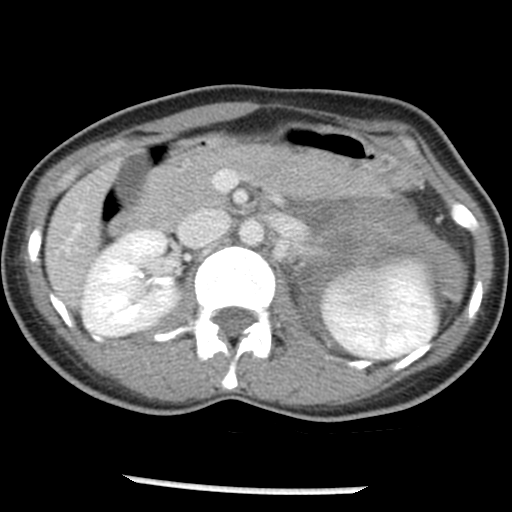
Contrast-enhanced abdominal CT, one axial slice. Slice 24 of 54 in the series (ordered by position). Intravenous contrast given. Soft-tissue window (W 400 / L 40 HU). 512 × 512 image matrix, field of view 240 × 240 mm. Female patient, age 33 years. From the clinical record (not read from this slice): diagnosis: adrenocortical carcinoma; tumour side: left adrenal; tumour size at pathology: 11 cm; Ki-67 index: 20 %; stage (as recorded): 2.
Annotated regions visible in this slice (semi-automatic segmentation, software-assisted and operator-edited):
- mass: bounding box <301,199,465,328> (left, top, right, bottom; pixels)